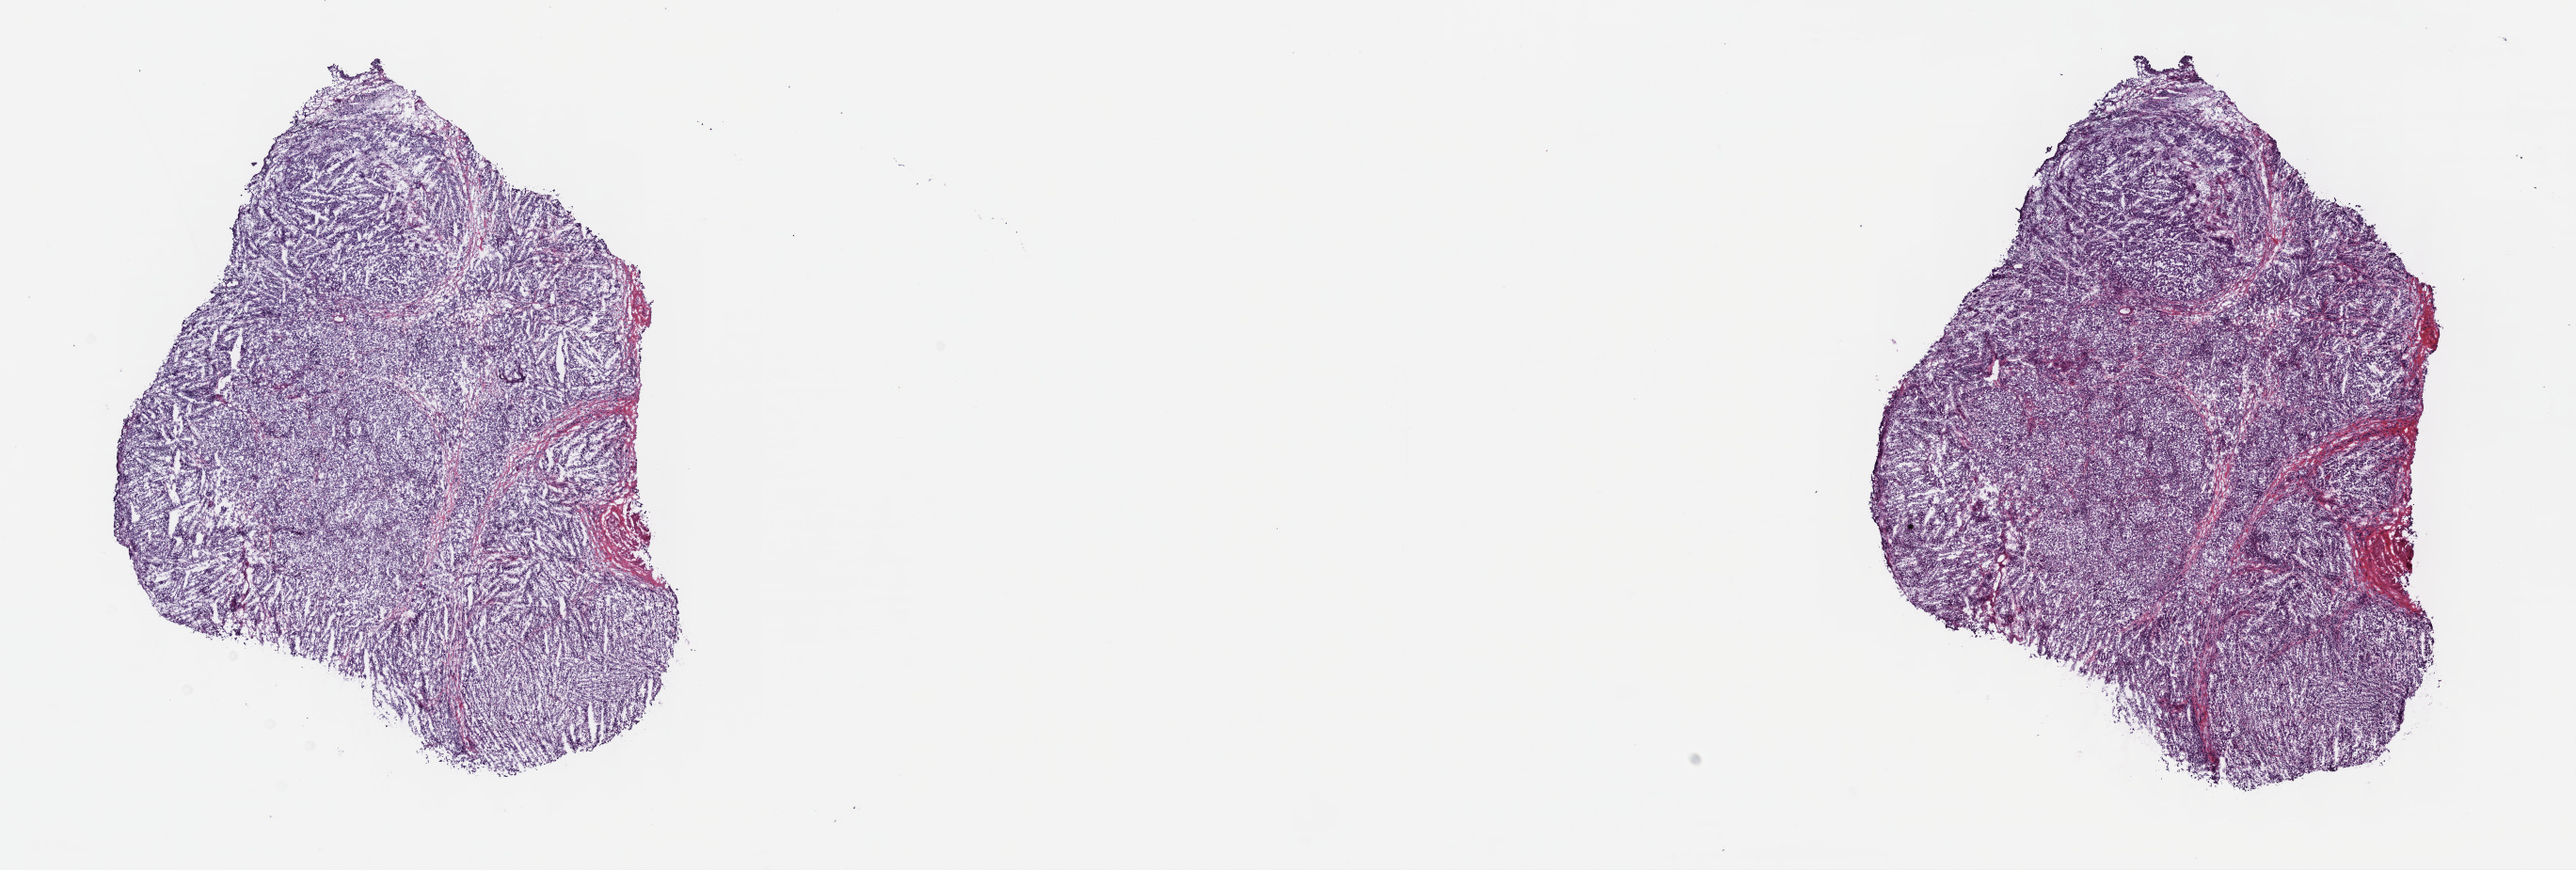
H&E whole-slide image, a low-resolution overview of the entire scanned area, about 22.1 x 7.5 mm (from a 40x scan). Frozen section from the top of the tissue portion. Primary tumour sample from the bladder. Male patient; age at initial diagnosis 79 years. Histologic grade: high grade. Pathologist review of this section (percent, as recorded): tumour cells 75%, tumour nuclei 75%, normal cells 0%, stromal cells 25%, necrosis 0%. Inflammatory infiltration, as recorded: lymphocyte infiltration 3%, monocyte infiltration 1%, neutrophil infiltration 5%.
Pathologic diagnosis: Transitional cell carcinoma. AJCC pathologic stage: III (7th edition).